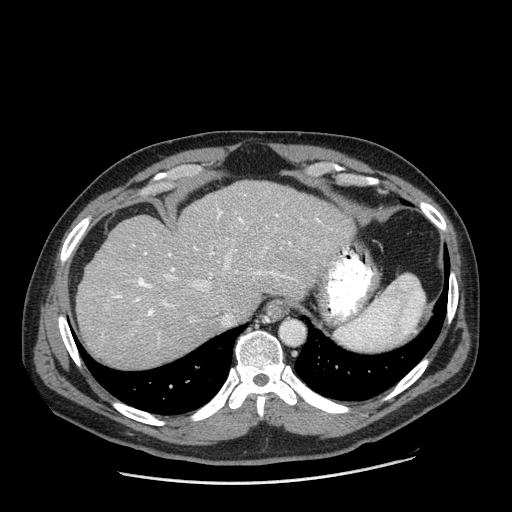
Contrast-enhanced abdominal CT (liver protocol), one axial slice; position 151 of 198 along the scan axis; 120 kVp; one of 2 acquisitions stored at this slice position; soft-tissue window (W 400 / L 40 HU); 2.5 mm slice thickness; 512 × 512 image matrix, field of view 400 × 400 mm. From the clinical record (not read from this slice): diagnosis: hepatocellular carcinoma (patient treated with transarterial chemoembolisation; whether this scan precedes or follows treatment is not stated here); TNM stage (as recorded): Stage-II; Child-Pugh class: A; tumour differentiation: moderately differentiated.
Outlined on this slice (semi-automatically segmented with operator editing):
- abdominal aorta: box from (x=281, y=322) to (x=303, y=344) px
- liver parenchyma outside the tumour (the mass and vessels are separate outlines, so this box may not span the whole liver): (x=76, y=180)–(x=354, y=368)
- liver vessels: (x=111, y=209)–(x=332, y=325)